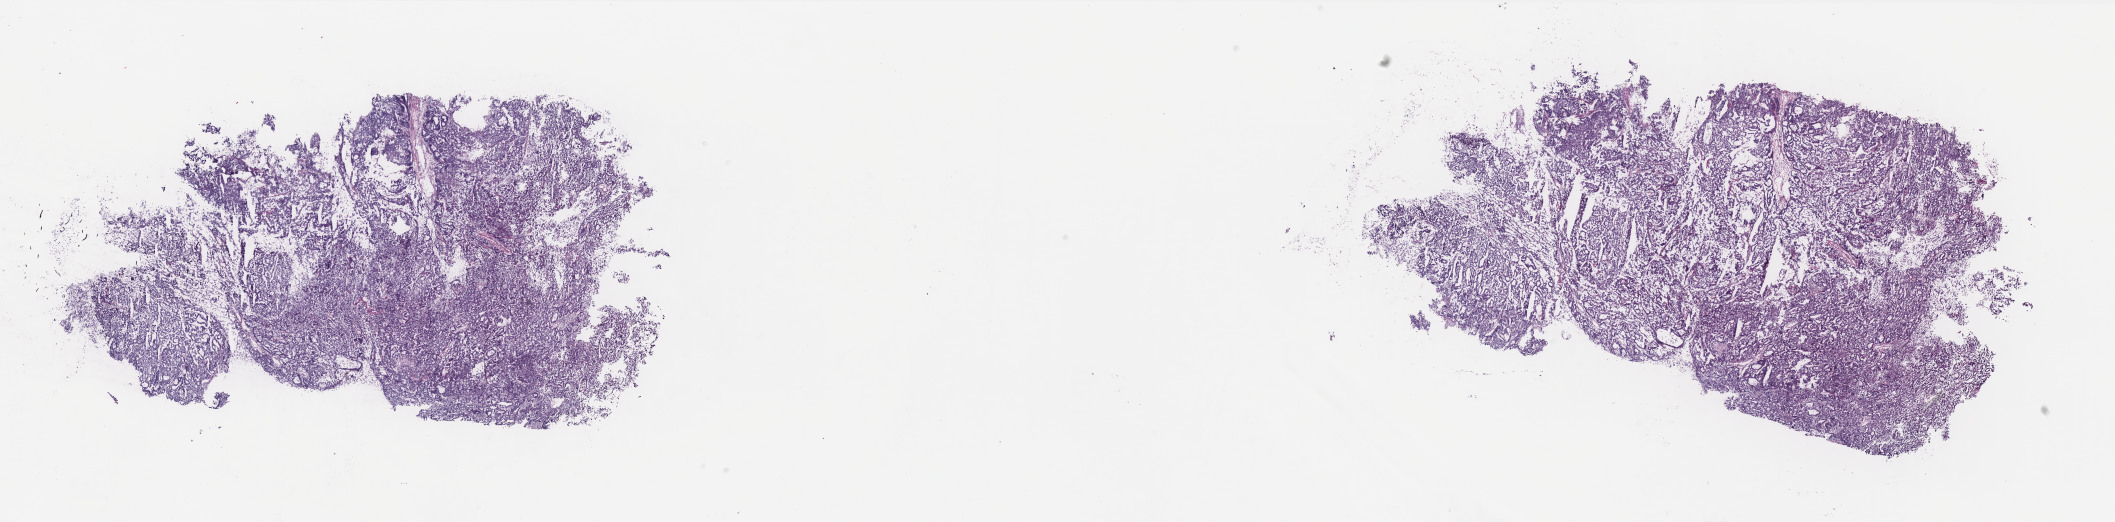
Hematoxylin and eosin (H&E) stained whole-slide image — shown as a low-resolution overview of the whole scanned area (about 33.9 x 8.4 mm, acquisition: 40x scan), frozen section from the top of the tissue portion, sample: primary tumour, uterus. Patient: female, age at initial diagnosis 62 years. Composition of this section per pathologist review: tumour cells 97%, tumour nuclei 90%.
Diagnosis: Endometrioid adenocarcinoma, NOS (endometrium).